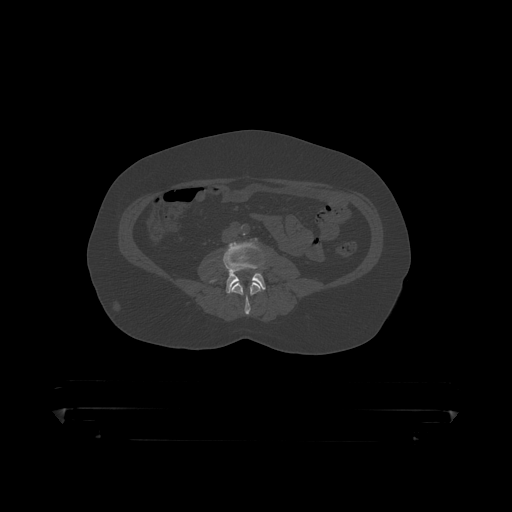
CT including the spine, one axial slice. Slice 76 of 390 in the series (ordered by position). 120 kVp. Bone window (W 1800 / L 400 HU). 1.25 mm slice thickness. 512 × 512 image matrix. Male patient, age 60 years. Case-level facts recorded for this patient, not image findings: primary cancer: prostate.
Outlined on this slice (semi-automatic segmentation, software-assisted and operator-edited):
- L3 vertebra: bounding box (x1, y1, x2, y2) in pixels: (231, 281, 262, 315)
- L4 vertebra: (211, 243, 266, 294)